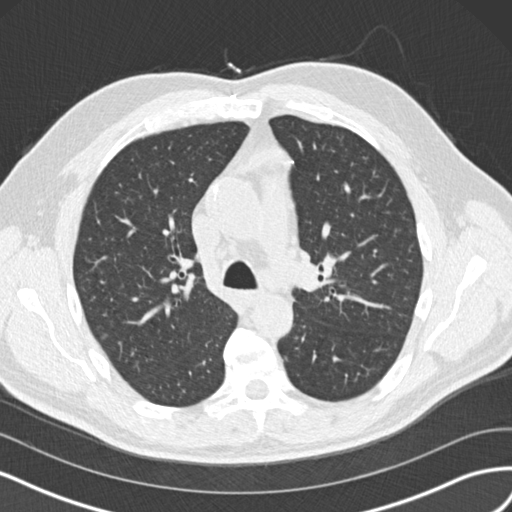
Low-dose screening chest CT, axial slice; baseline annual screen; lung window (W 1500 / L -600 HU); 2 mm slice thickness; standard (soft-tissue) reconstruction kernel (B30f). Male participant, aged 65 years at enrolment.
Expert-annotated lung lesion, bounding box <305,242,353,296> (left, top, right, bottom; pixels). The screening reader recorded 4 non-calcified nodules or masses ≥4 mm on this exam; which of them this box marks is not recorded. Official screen result: positive, change unspecified: nodule(s) >= 4 mm or enlarging nodule(s), mass(es), or other non-specific abnormalities suspicious for lung cancer. Participant outcome: lung cancer diagnosed 945 days after this screen (after the third annual screen) — acinar cell carcinoma, left upper lobe, stage IA (AJCC 6th edition), 25 mm at pathology.